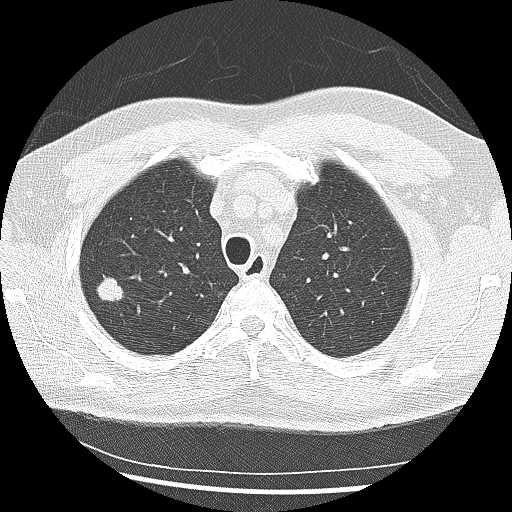
Low-dose screening chest CT, one axial slice; position 209 of 265 along the scan axis; reconstruction kernel LUNG; 120 kVp; lung window (W 1500 / L -600 HU); 2.5 mm slice thickness; 512 × 512 image matrix, field of view 340 × 340 mm.
Outlined on this slice (manually delineated by an expert):
- lesion 1 (tumor, upper lobe of right lung): bounding box [x1, y1, x2, y2] px = [97, 275, 124, 301]